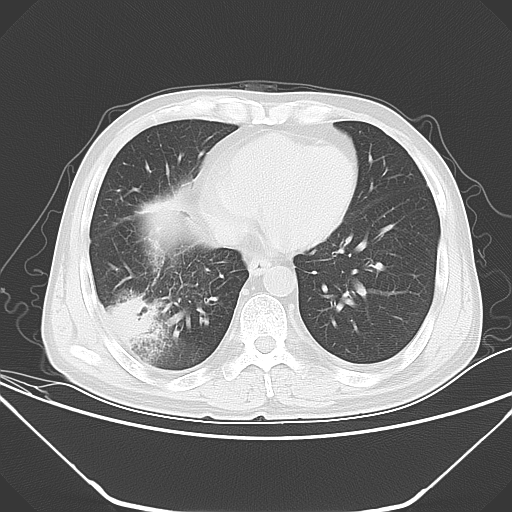
Chest CT, one axial slice; position 16 of 52 along the scan axis; 120 kVp; lung window (W 1500 / L -600 HU); 5 mm slice thickness; 512 × 512 image matrix, field of view 379 × 379 mm. Patient: male, 54 years. From the clinical record (not read from this slice): clinical TNM (as recorded): T2 N1 M0.
Outlined on this slice (rectangle marked by the reading radiologist):
- lung tumour (recorded histology: adenocarcinoma): bounding box <105,290,158,346> (left, top, right, bottom; pixels)